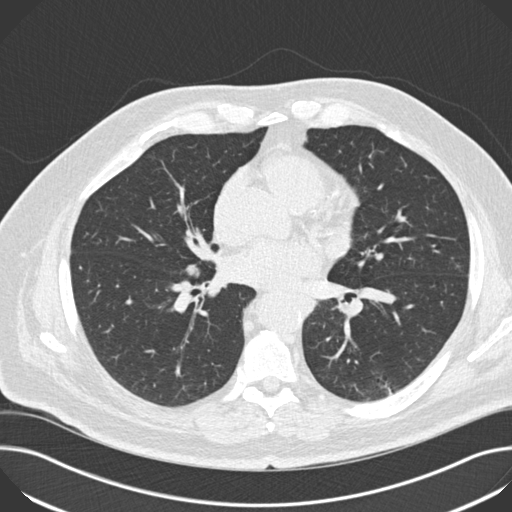
Chest CT (low-dose screening protocol), one axial image. Third screening round (two years after baseline). Lung window (W 1500 / L -600 HU). 2 mm slice thickness. 120 kVp. Slice 85 of 172 in the series. Male participant, aged 68 years at enrolment. Current smoker at enrolment.
Lesion marked by an expert reader, box from (x=165, y=233) to (x=229, y=303) px. No non-calcified nodule or mass ≥4 mm was recorded by the screening reader at this exam.